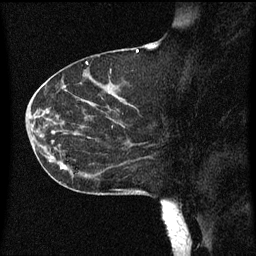
Breast MRI (dynamic contrast-enhanced), one sagittal slice; position 27 of 60 along the scan axis; dynamic contrast-enhanced series, image 2 of 3 at this slice position (ordered by acquisition); 1.5 T; TE 4.2 ms, TR 8 ms; 2 mm slice thickness; 256 × 256 image matrix, field of view 200 × 200 mm. Female patient, age 55 years.
Structures marked on this image (semi-automatic segmentation, software-assisted and operator-edited):
- analysis volume of interest (the breast-tissue region the enhancement analysis was run in; not a lesion): bounding box <46,124,151,183> (left, top, right, bottom; pixels)
- tumour enhancement mask (voxels above the 70 % enhancement threshold inside the analysis volume of interest): <50,126,147,165>